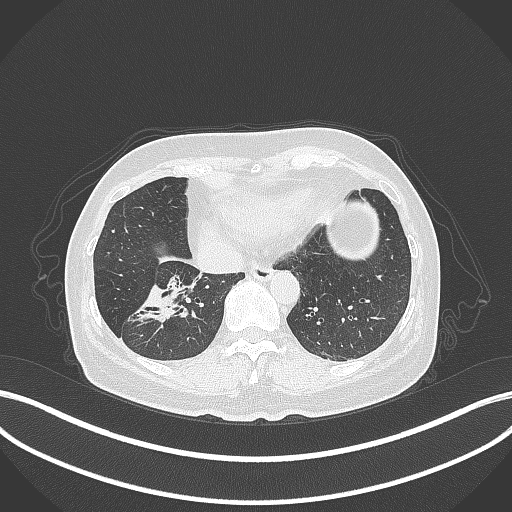
Chest CT, one axial slice; slice 112 of 429 in the series (ordered by position); reconstruction kernel B70f; lung window (W 1500 / L -600 HU); 1 mm slice thickness; 512 × 512 image matrix, field of view 400 × 400 mm. Female patient, age 67 years. From the clinical record (not read from this slice): clinical TNM (as recorded): T1c N1 M0; histopathological grade: G2-3.
Structures marked on this image (bounding box drawn by a radiologist):
- lung tumour (recorded histology: adenocarcinoma): bounding box <128,276,192,329> (left, top, right, bottom; pixels)